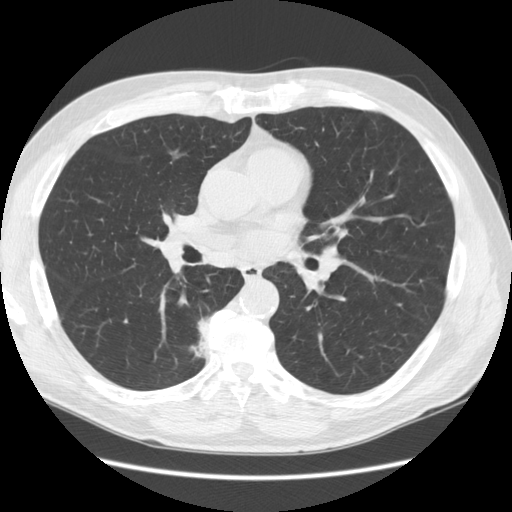
Low-dose screening chest CT, axial slice, second screening round (one year after baseline), lung window (W 1500 / L -600 HU), standard (soft-tissue) reconstruction kernel (STANDARD), slice 64 of 133 in the series. Male participant, aged 69 years at enrolment. Former smoker at enrolment.
- Lesion marked by an expert reader, bounding box (x1, y1, x2, y2) in pixels: (168, 306, 235, 372).
- The screening reader recorded 2 non-calcified nodules or masses ≥4 mm on this exam; which of them this box marks is not recorded.
- Participant outcome: lung cancer diagnosed 88 days after this screen — bronchiolo-alveolar adenocarcinoma, NOS, right lower lobe, well differentiated (G1), stage IB (AJCC 6th edition), 23 mm at pathology.